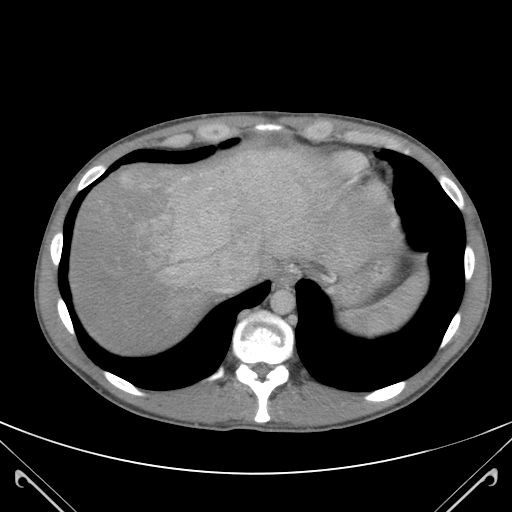
Contrast-enhanced abdominal CT (liver protocol), one axial slice; position 101 of 118 along the scan axis; 120 kVp; soft-tissue window (W 400 / L 40 HU); 3 mm slice thickness; 512 × 512 image matrix, field of view 380 × 380 mm. Case-level facts recorded for this patient, not image findings: diagnosis: hepatocellular carcinoma (patient treated with transarterial chemoembolisation; whether this scan precedes or follows treatment is not stated here); TNM stage (as recorded): Stage-IIIB.
Structures marked on this image (semi-automatic segmentation, software-assisted and operator-edited):
- abdominal aorta: box from (x=273, y=289) to (x=295, y=312) px
- liver parenchyma outside the tumour (the mass and vessels are separate outlines, so this box may not span the whole liver): (x=74, y=151)–(x=327, y=353)
- mass: (x=118, y=155)–(x=309, y=286)
- liver vessels: (x=123, y=154)–(x=259, y=293)